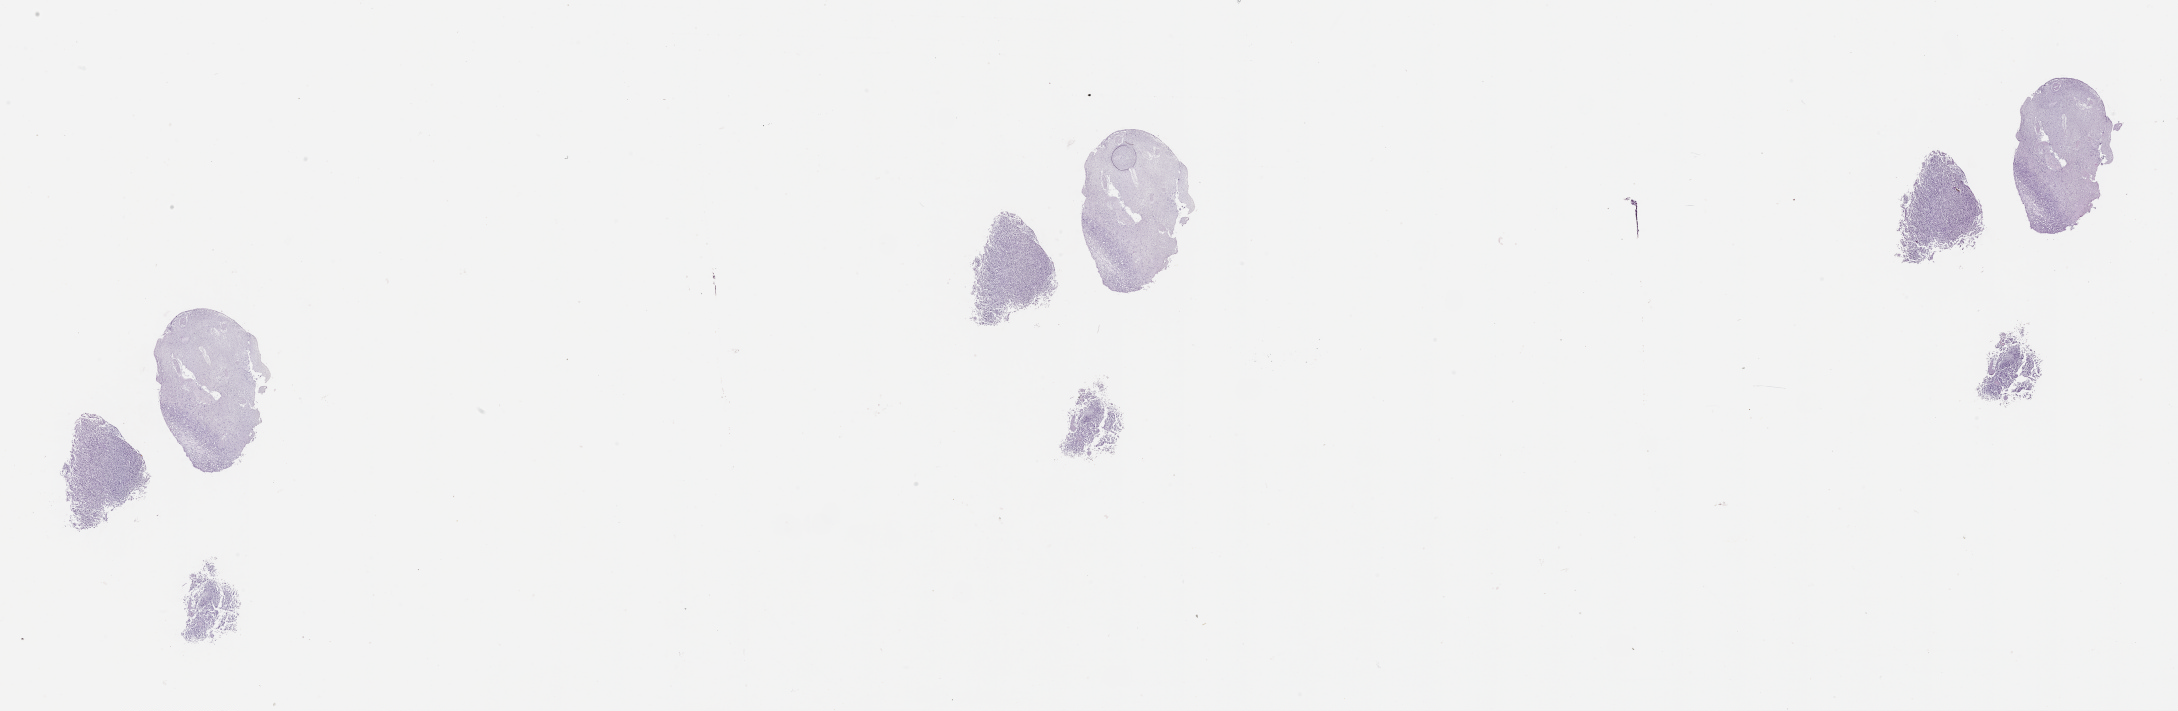
Whole-slide histology image, H&E-stained, a low-resolution overview of the entire scanned area, about 35.1 x 11.5 mm (from a 20x scan). Brain, tumour tissue. 81-year-old female patient.
Primary tumour site (as recorded): parietal lobe. Histologic diagnosis: Glioblastoma.